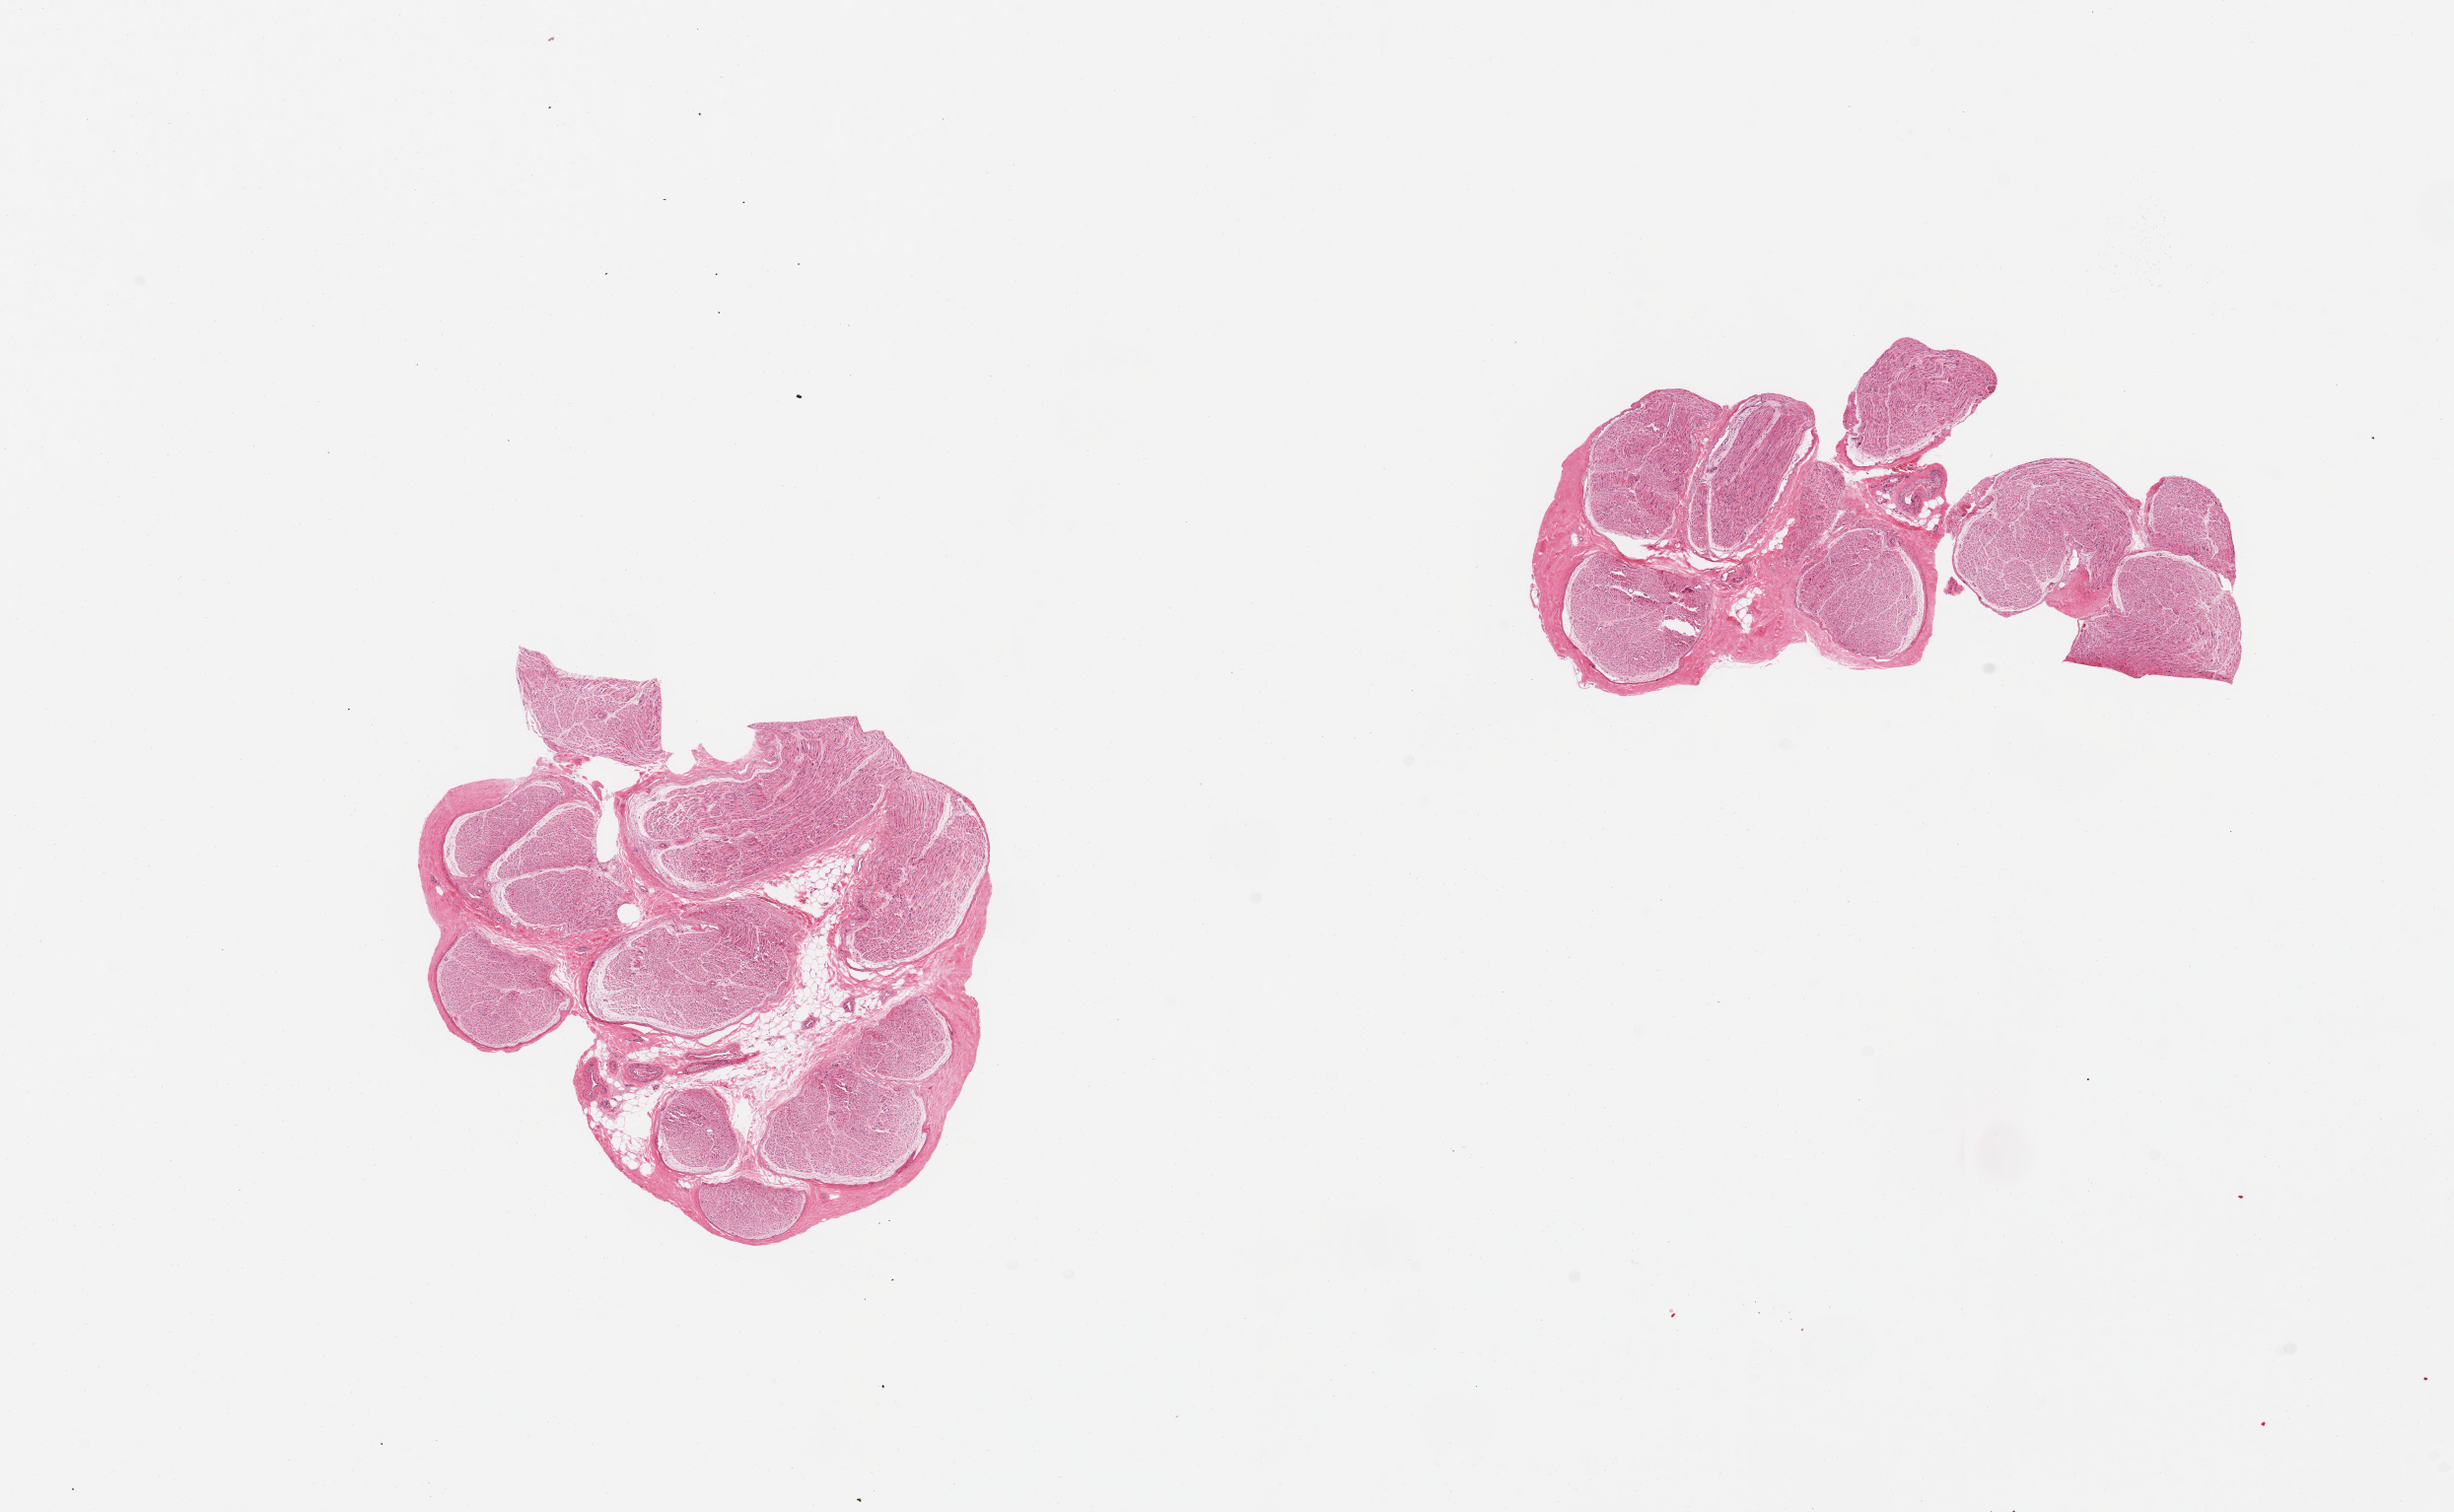
Whole-slide image, H&E stain, shown as a low-resolution overview of the whole scanned area (about 19.7 x 12.1 mm). PAXgene-fixed paraffin-embedded (PFPE) section. Section of tibial nerve (target tissue). Tissue donor sample. Donor sex: male.
Review note (as recorded): 2 pieces; one contains ~10% internal fat.